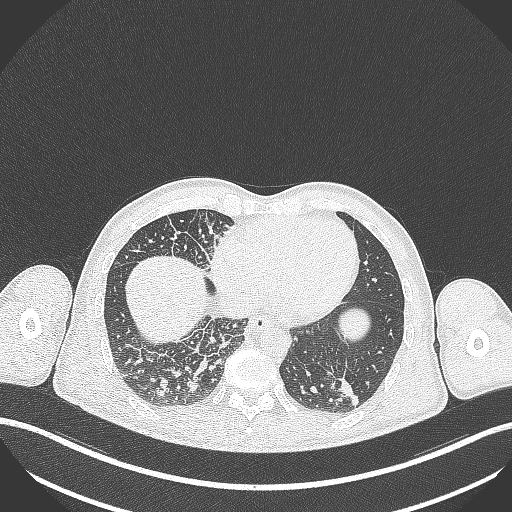
Chest CT, one axial slice; position 87 of 348 along the scan axis; reconstruction kernel B70f; 120 kVp; lung window (W 1500 / L -600 HU); 1 mm slice thickness; 512 × 512 image matrix, field of view 400 × 400 mm. Patient: male, 49 years. From the clinical record (not read from this slice): clinical TNM (as recorded): T2b N1 M0.
Annotated regions visible in this slice (rectangle marked by the reading radiologist):
- lung tumour (recorded histology: adenocarcinoma): box from (x=335, y=375) to (x=362, y=410) px